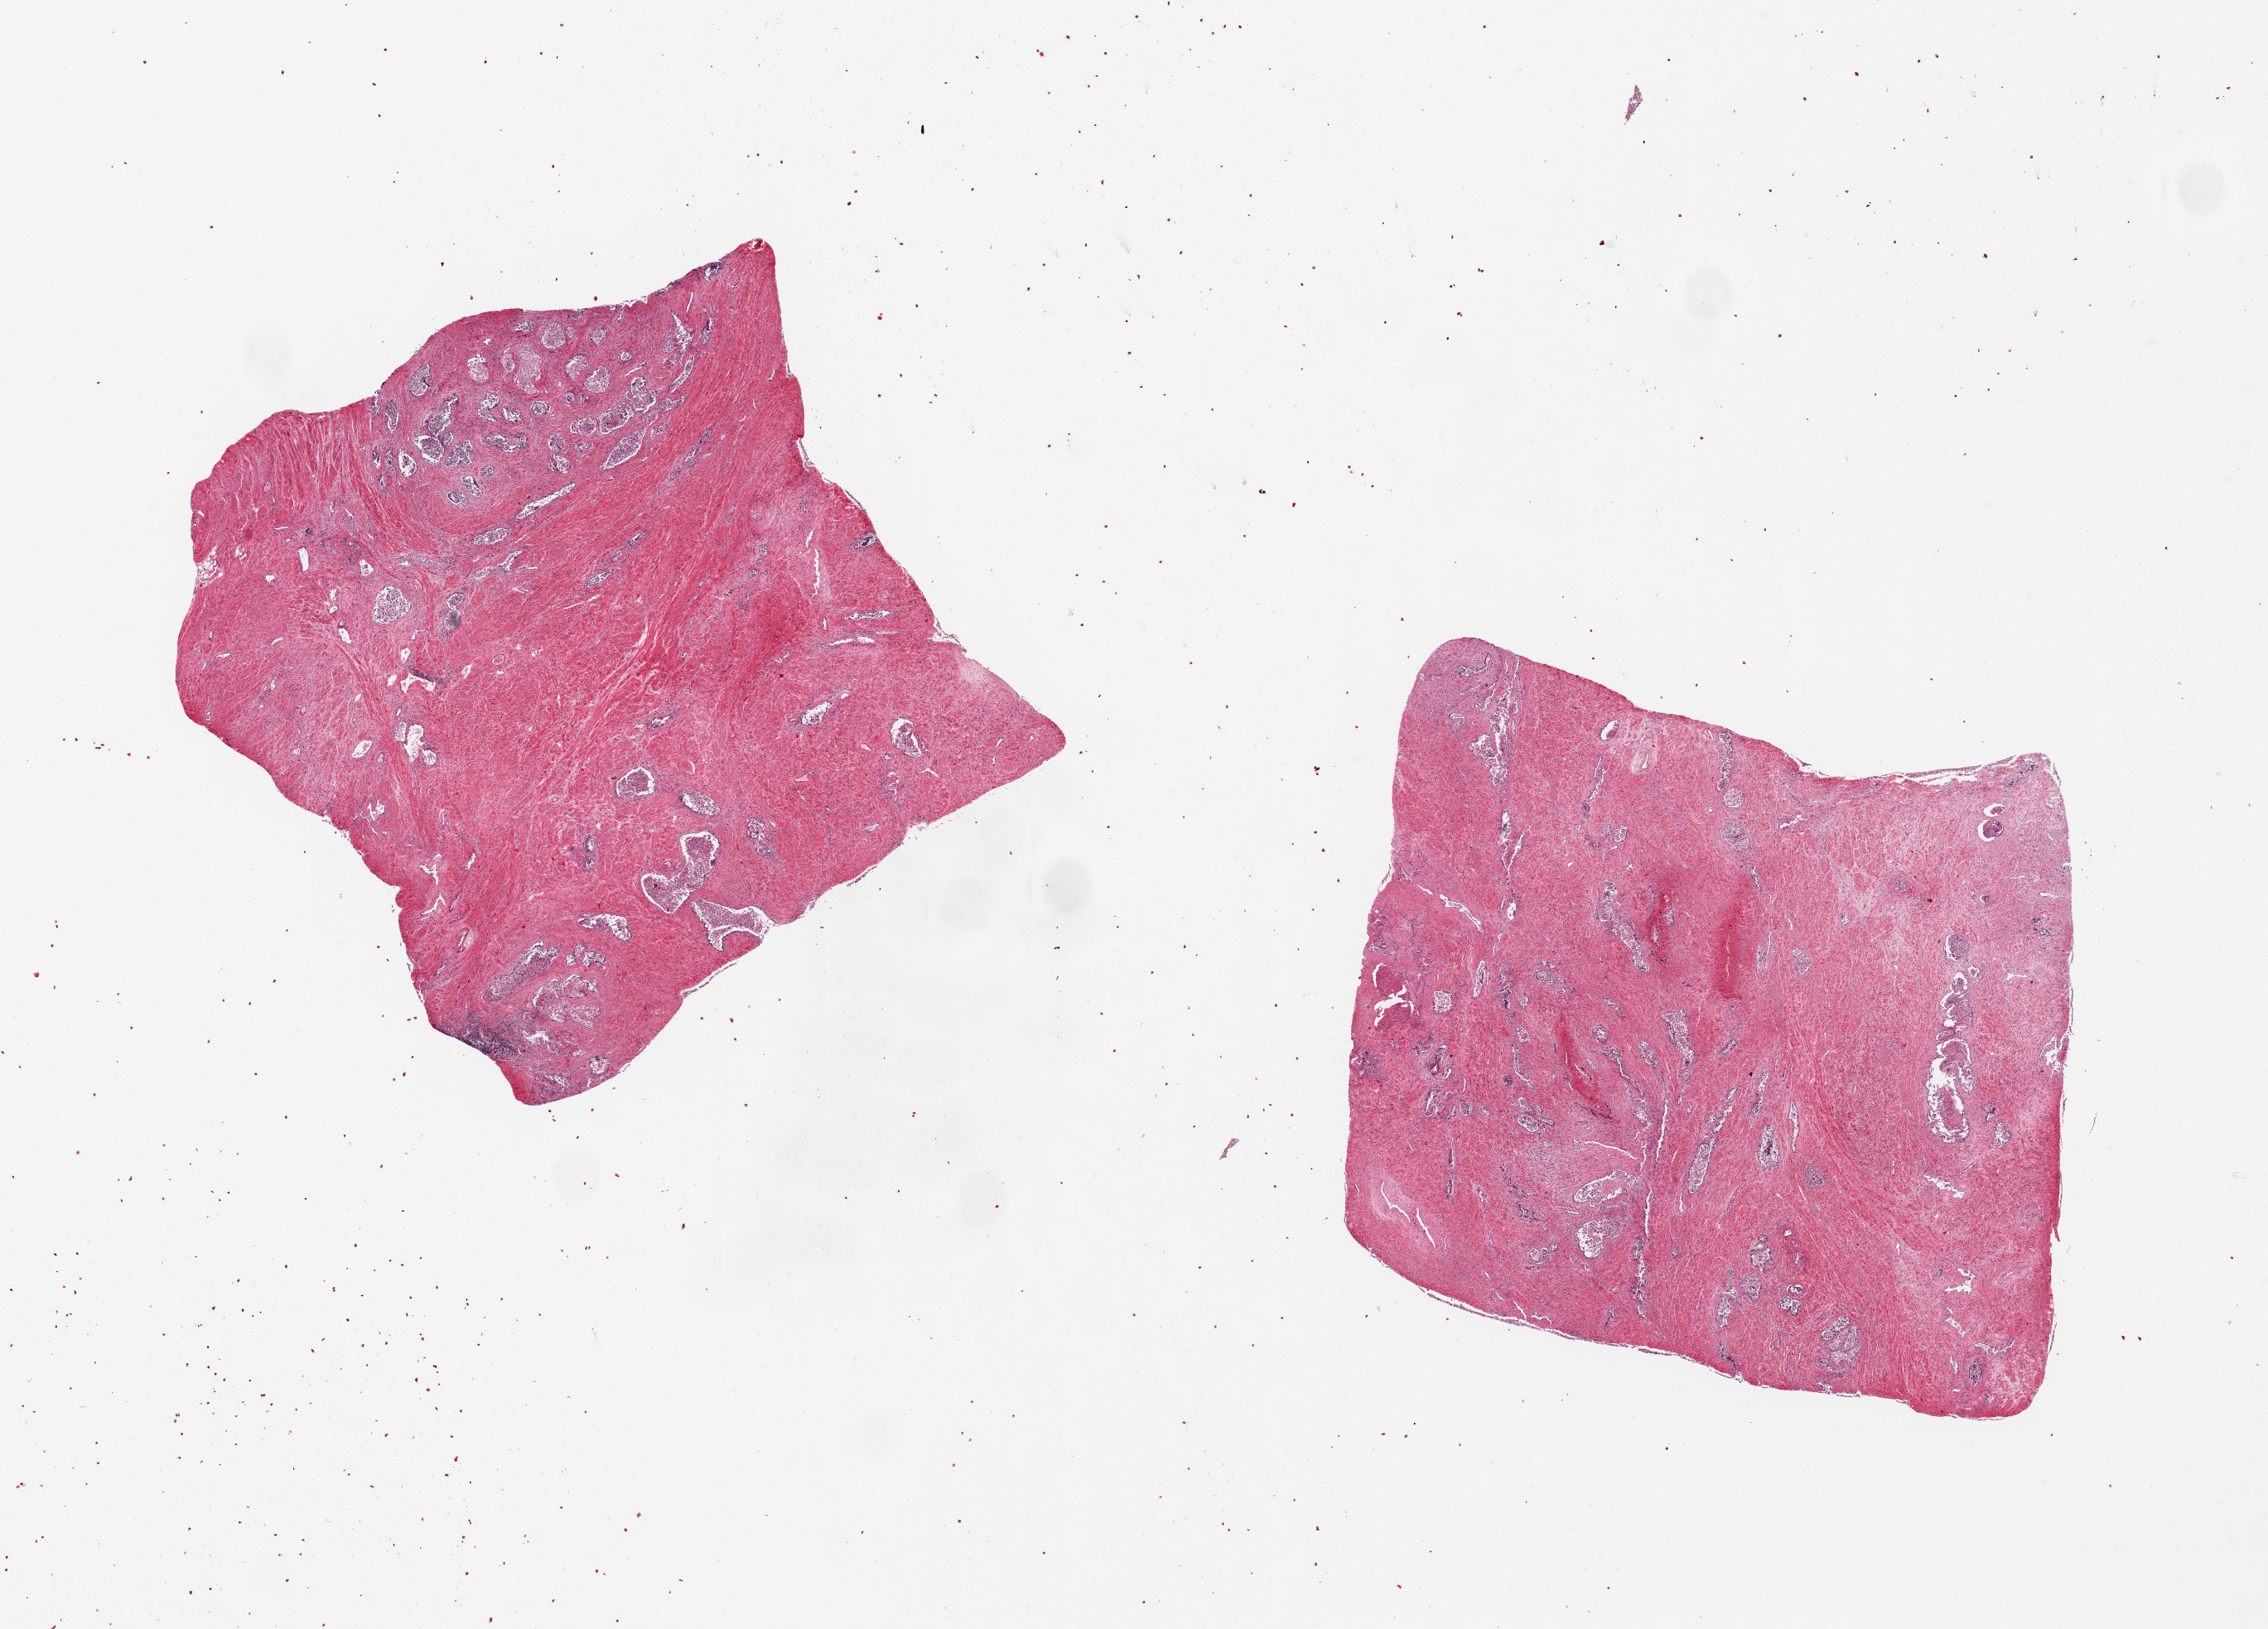
Hematoxylin and eosin (H&E) whole-slide image — shown as a low-resolution overview of the whole scanned area (about 21.7 x 15.6 mm); PAXgene-fixed, paraffin-embedded tissue; section of prostate (target tissue); donor tissue sample.
* review note (as recorded): 2 pieces, 7x6.3 & 6.6x6.2mm; glands autolyzed, stroma OK; more stroma than glands